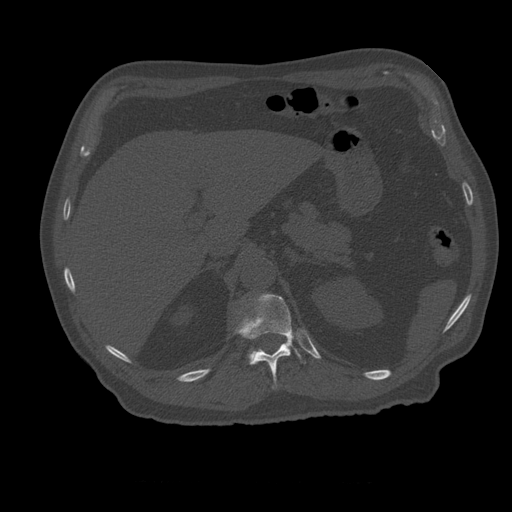
CT including the spine, one axial slice; slice 258 of 399 in the series (ordered by position); reconstruction kernel STANDARD; 120 kVp; bone window (W 1800 / L 400 HU); 1.25 mm slice thickness; 512 × 512 image matrix, field of view 407 × 407 mm. Patient age 73 years. From the clinical record (not read from this slice): primary cancer: prostate; vertebrae with lytic lesions (as recorded): L2.
Structures marked on this image (semi-automatic segmentation, software-assisted and operator-edited):
- L1 vertebra: box from (x=239, y=323) to (x=252, y=365) px
- T12 vertebra: (x=236, y=294)–(x=302, y=384)